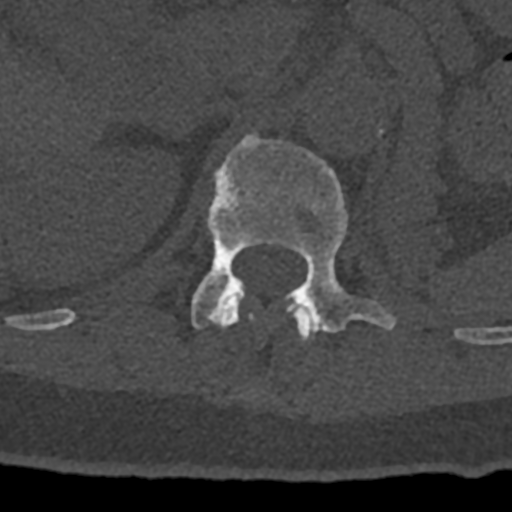
CT including the spine, one axial slice; position 452 of 797 along the scan axis; reconstruction kernel Br40s/3; bone window (W 1800 / L 400 HU); 512 × 512 image matrix, field of view 160 × 160 mm. Male patient, age 74 years. Case-level facts recorded for this patient, not image findings: primary cancer: renal.
Annotated regions visible in this slice (semi-automatic segmentation, software-assisted and operator-edited):
- L1 vertebra: box from (x=191, y=133) to (x=396, y=333) px
- T12 vertebra: (x=70, y=298)–(x=315, y=341)